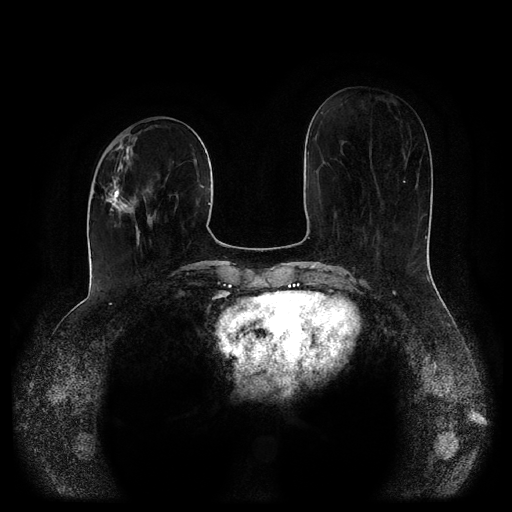
Breast MRI (dynamic contrast-enhanced, multi-phase), one axial slice; dynamic contrast-enhanced series, time point 2 of 5 at this slice position (early post-contrast); 1.5 T; TE 2.6 ms, TR 5.2 ms; 512 × 512 image matrix, field of view 380 × 380 mm. Patient: female, 52 years.
Structures marked on this image (semi-automatically segmented with operator editing):
- breast lesion (labelled 'tumour' in the annotation; benign lesions carry a separate 'benign' label): bounding box [x1, y1, x2, y2] px = [103, 145, 135, 222]